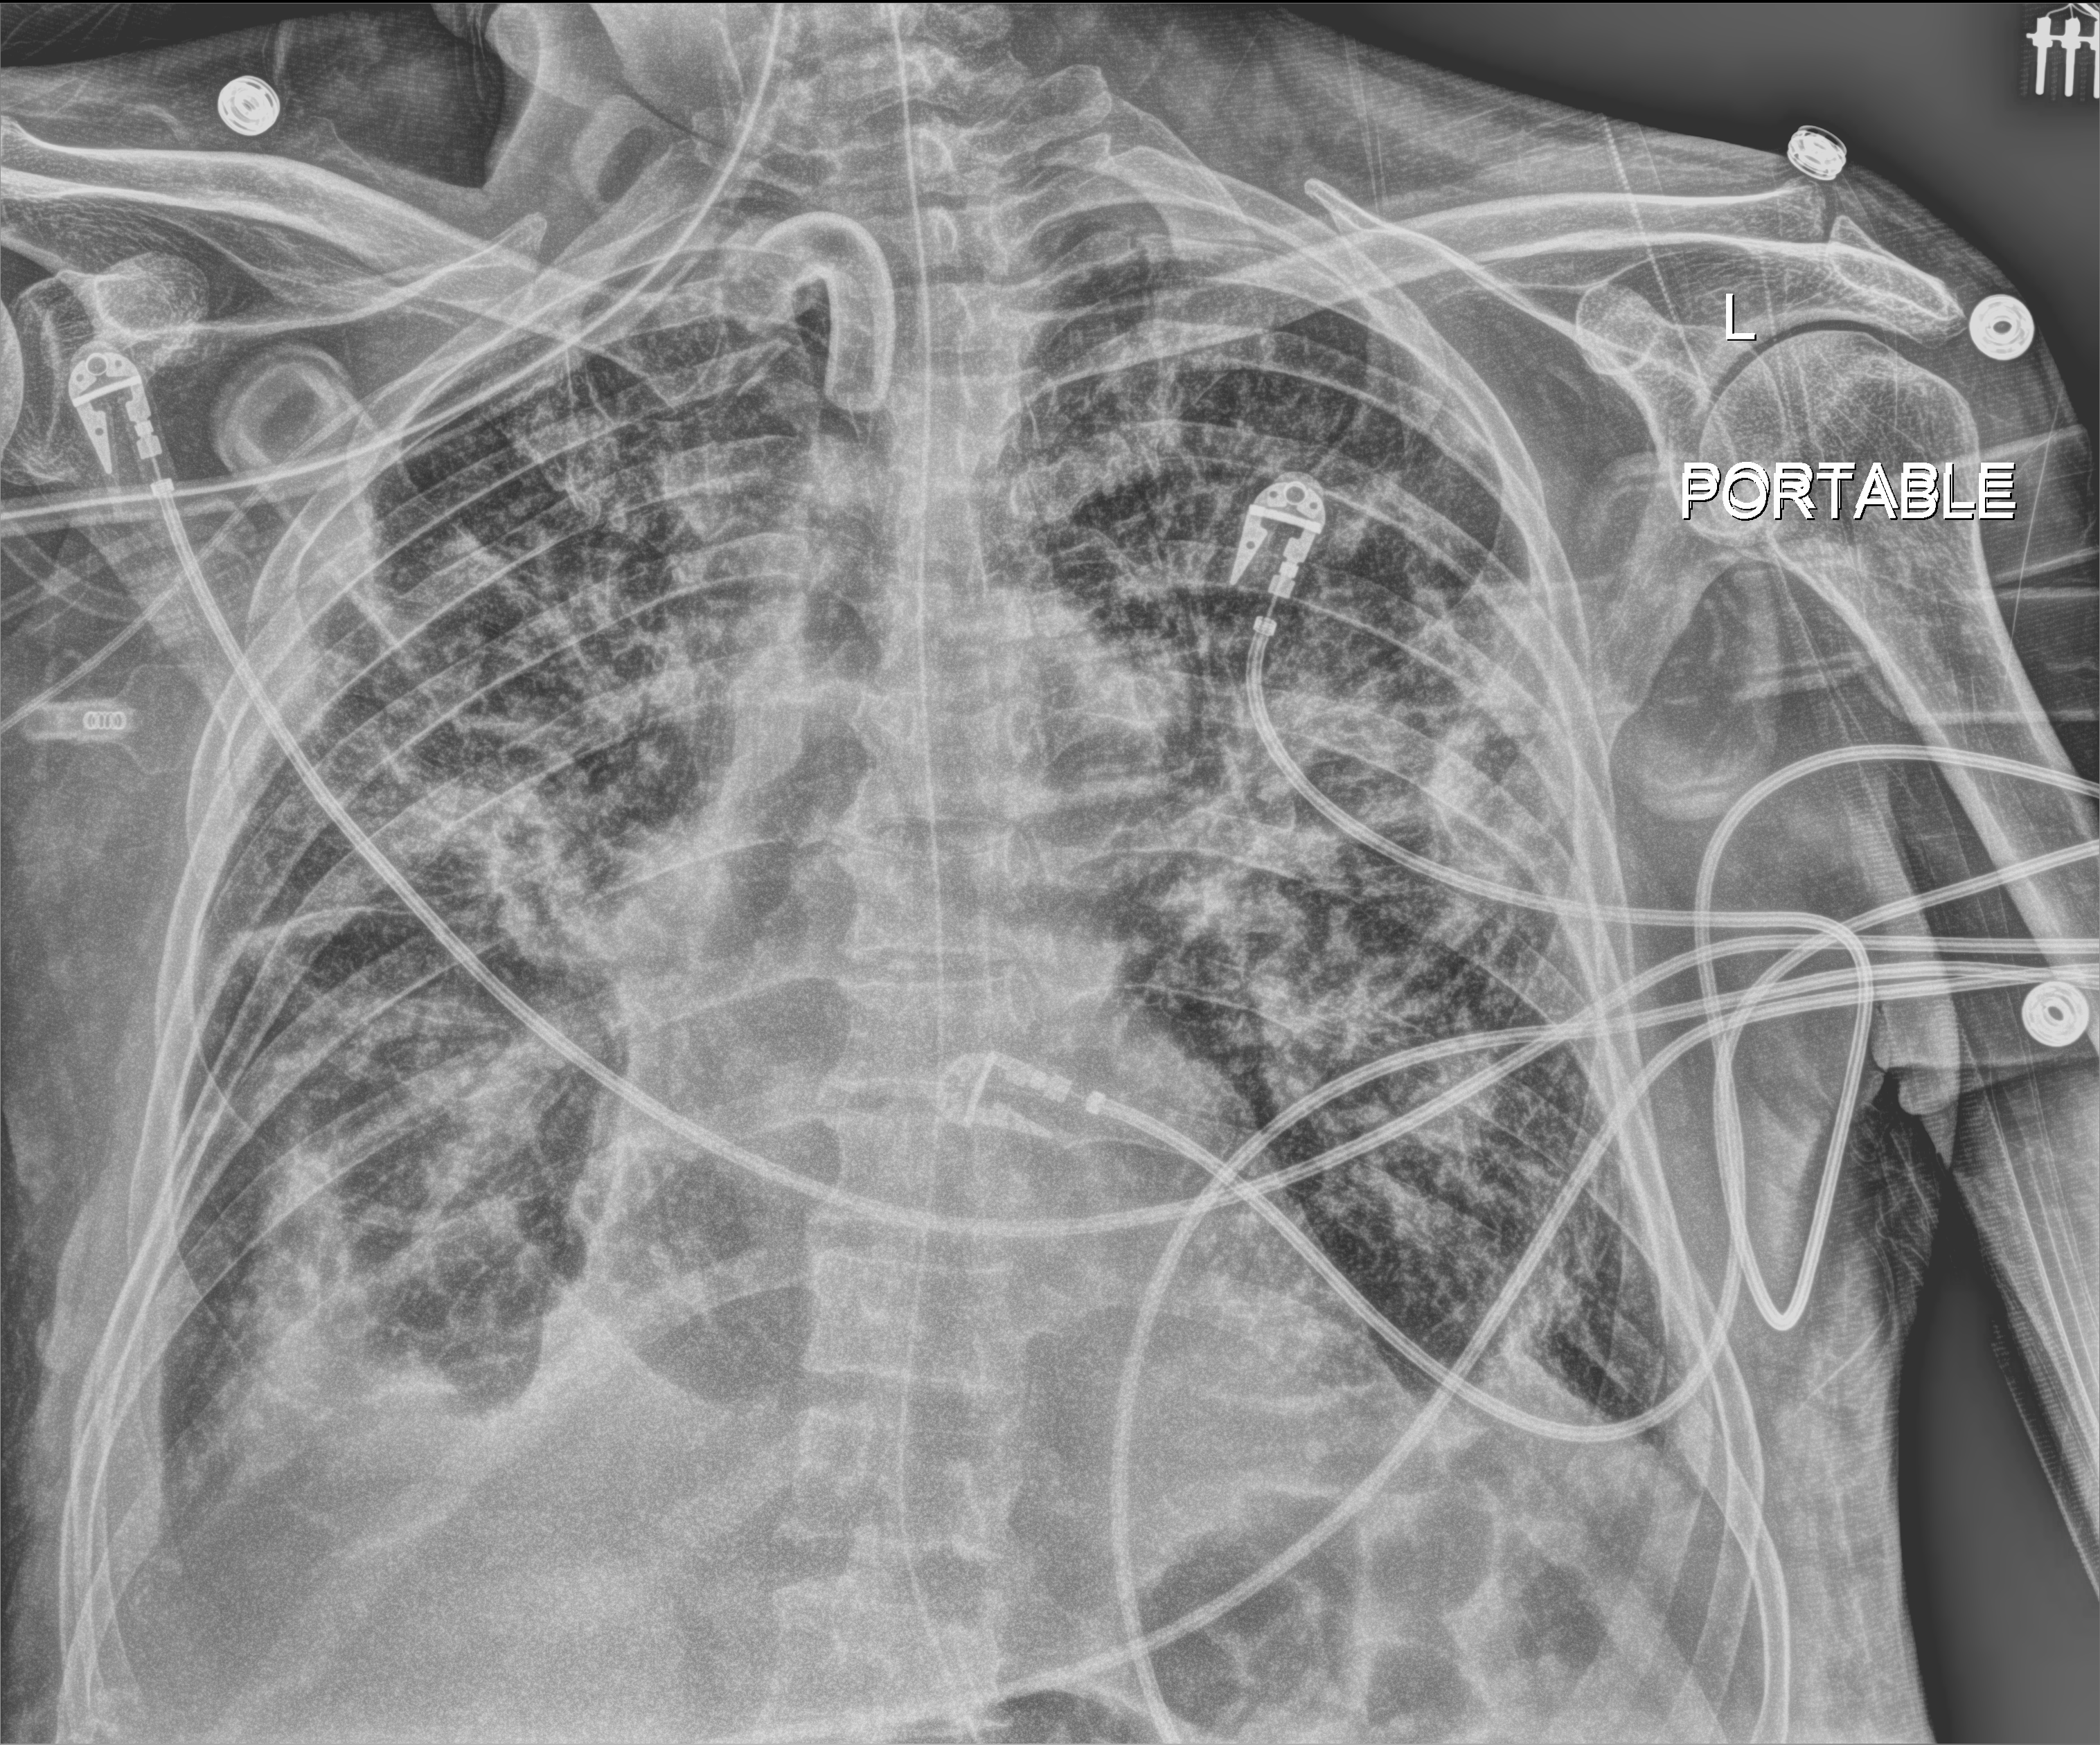
Portable chest radiograph; anteroposterior (AP) projection. Male patient hospitalised with COVID-19, age 75–90 years.
From the hospital-stay record, not from the radiograph (when in the stay this image was taken is not recorded): mechanically ventilated during this hospital stay: yes; admitted to intensive care during this hospital stay: yes; COPD (admission record): no.